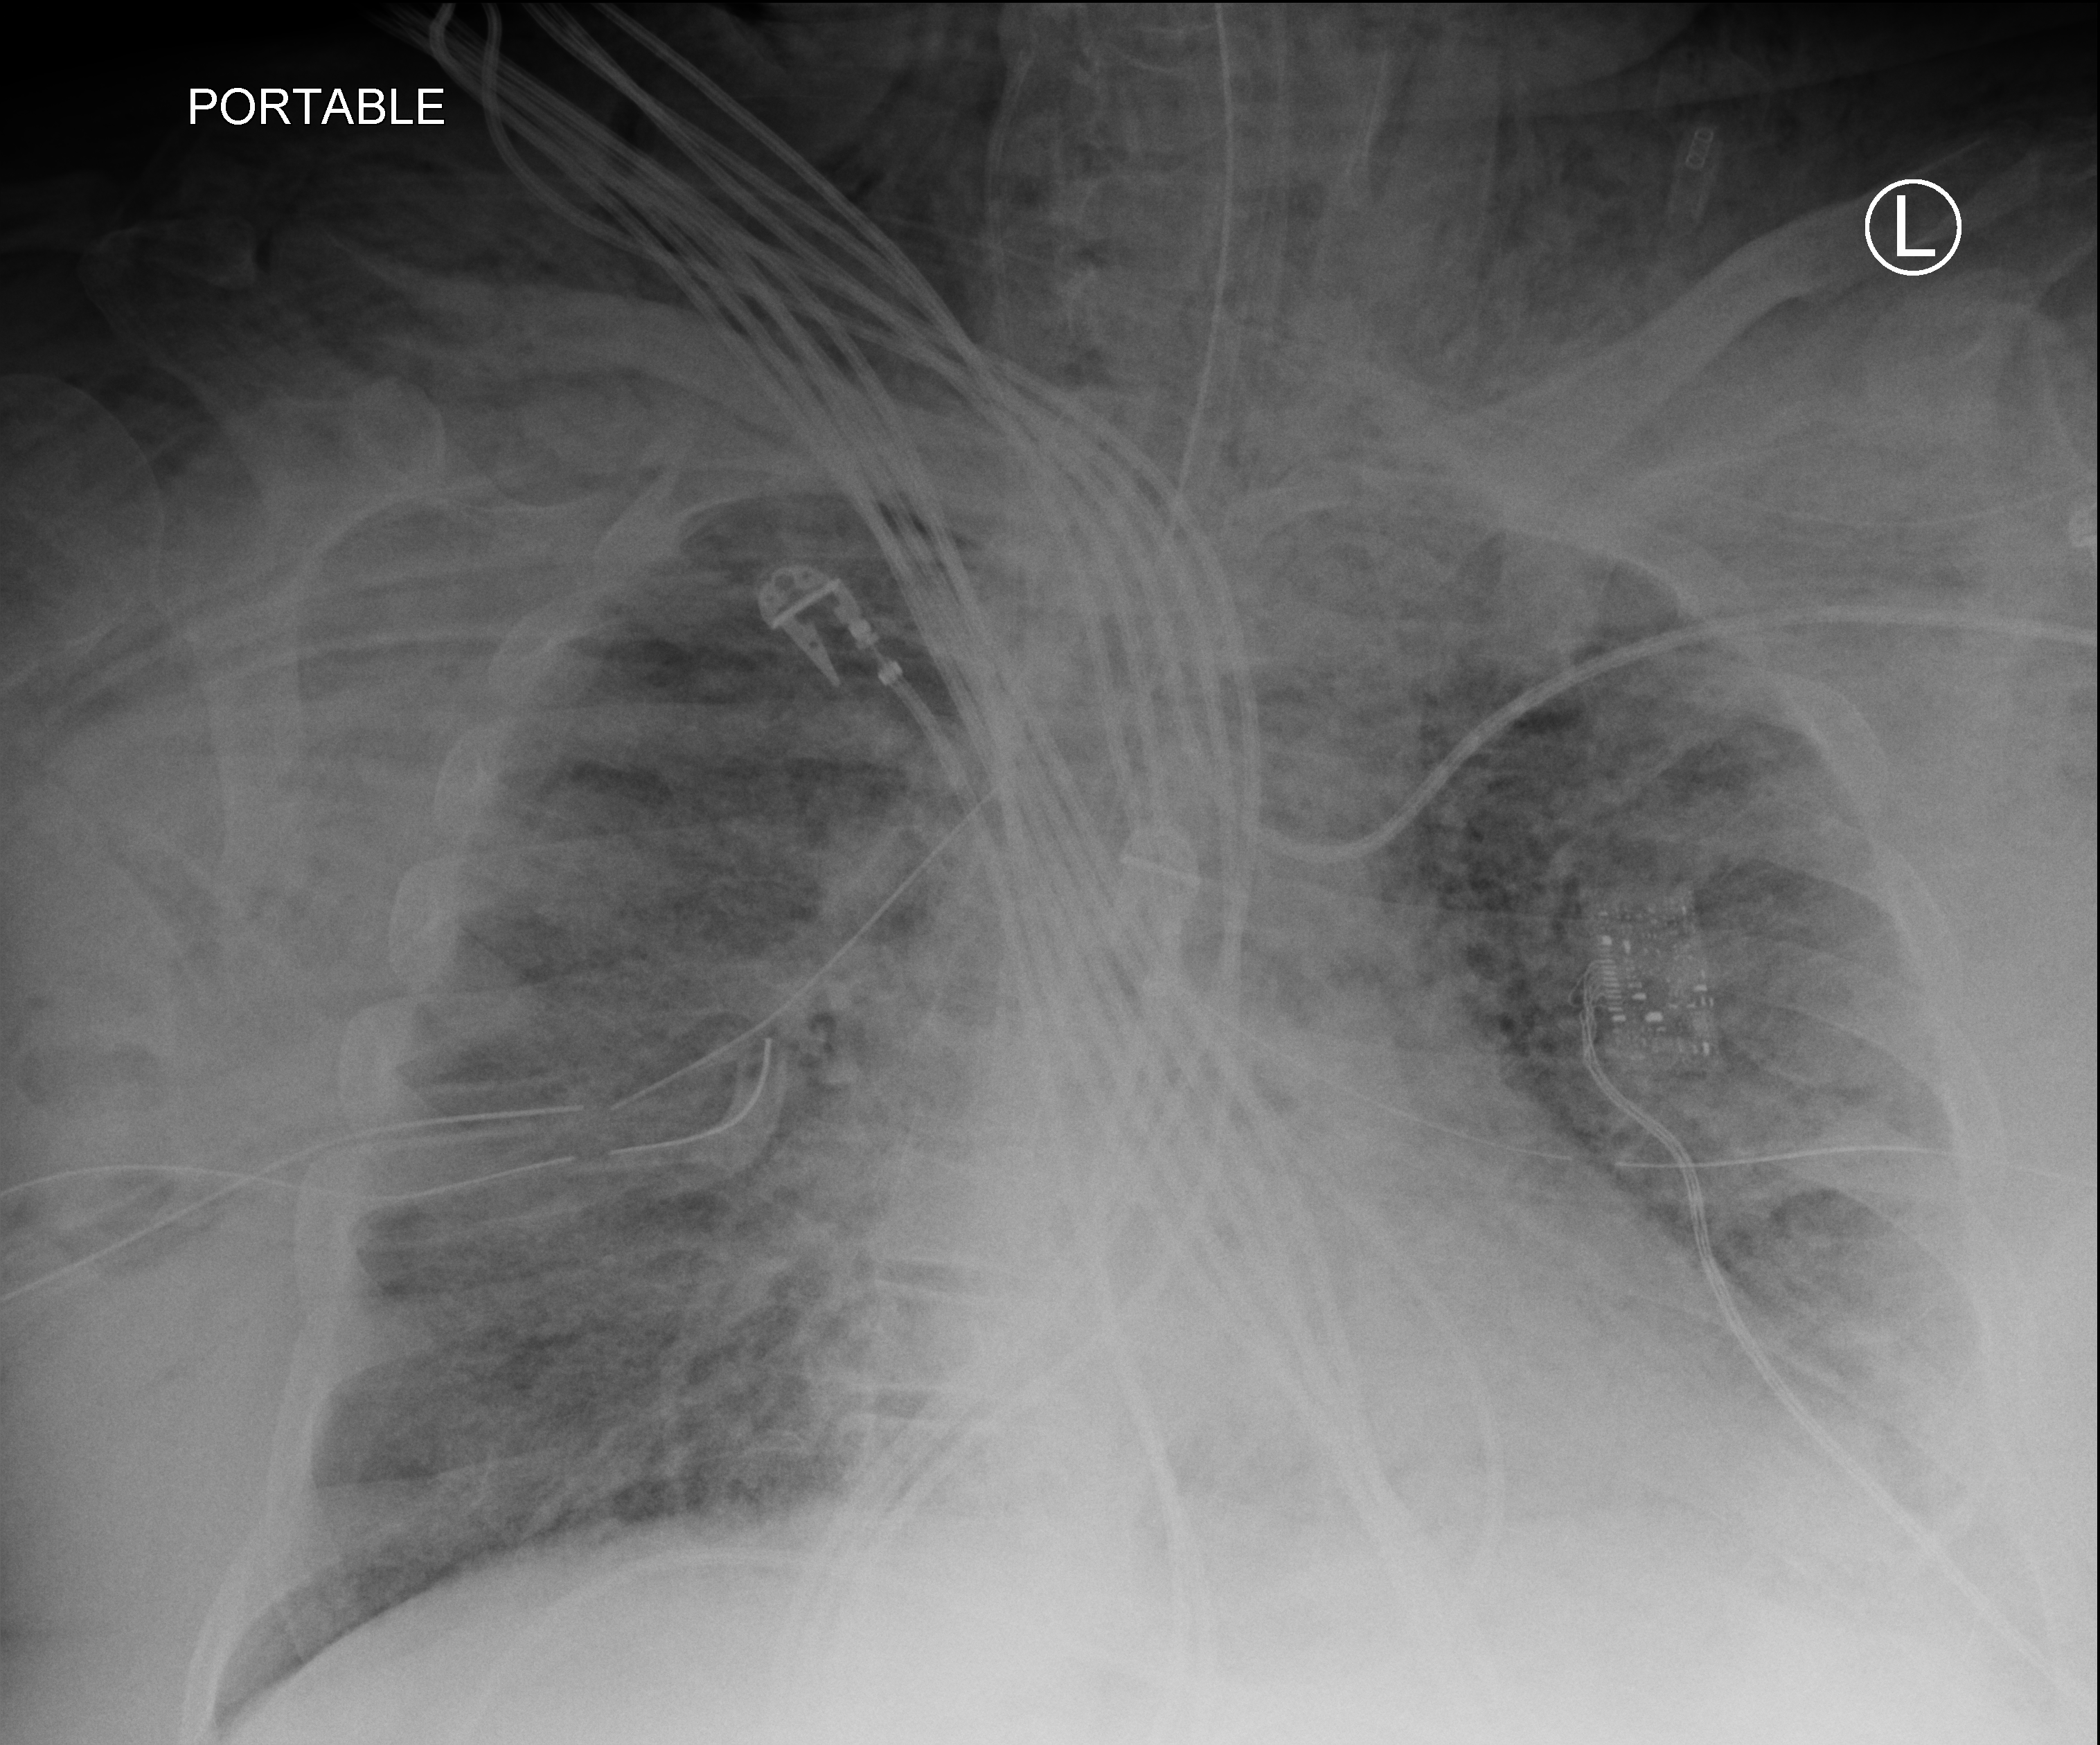
Bedside chest radiograph (computed radiography), anteroposterior (AP) projection. Patient hospitalised with COVID-19, aged 18–59 years.
Hospital-stay facts (about this admission, not read from this image; timing relative to this image not recorded):
- mechanically ventilated during this hospital stay: yes
- length of hospital stay: 26 days
- admitted to intensive care during this hospital stay: yes